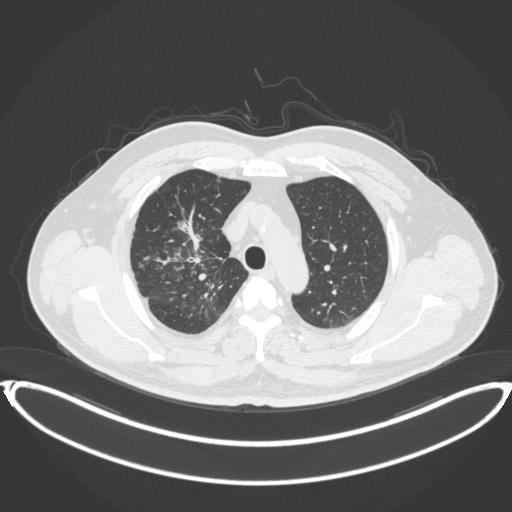
Chest CT, one axial slice. Slice 295 of 399 in the series (ordered by position). Reconstruction kernel B31f. 120 kVp. Lung window (W 1500 / L -600 HU). 1 mm slice thickness. 512 × 512 image matrix, field of view 445 × 445 mm. Male patient, age 53 years. From the clinical record (not read from this slice): clinical TNM (as recorded): T2a N0 M0.
Structures marked on this image (rectangle marked by the reading radiologist):
- lung tumour (recorded histology: adenocarcinoma): box from (x=174, y=213) to (x=194, y=236) px